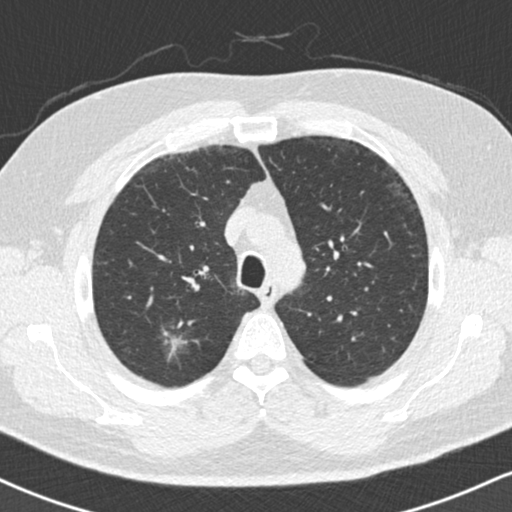
Low-dose screening chest CT, one axial slice. Position 127 of 169 along the scan axis. Reconstruction kernel B30f. Lung window (W 1500 / L -600 HU). 2 mm slice thickness. 512 × 512 image matrix, field of view 320 × 320 mm.
Structures marked on this image (manually delineated by an expert):
- lesion 1 (tumor, upper lobe of right lung): box from (x=164, y=333) to (x=187, y=356) px